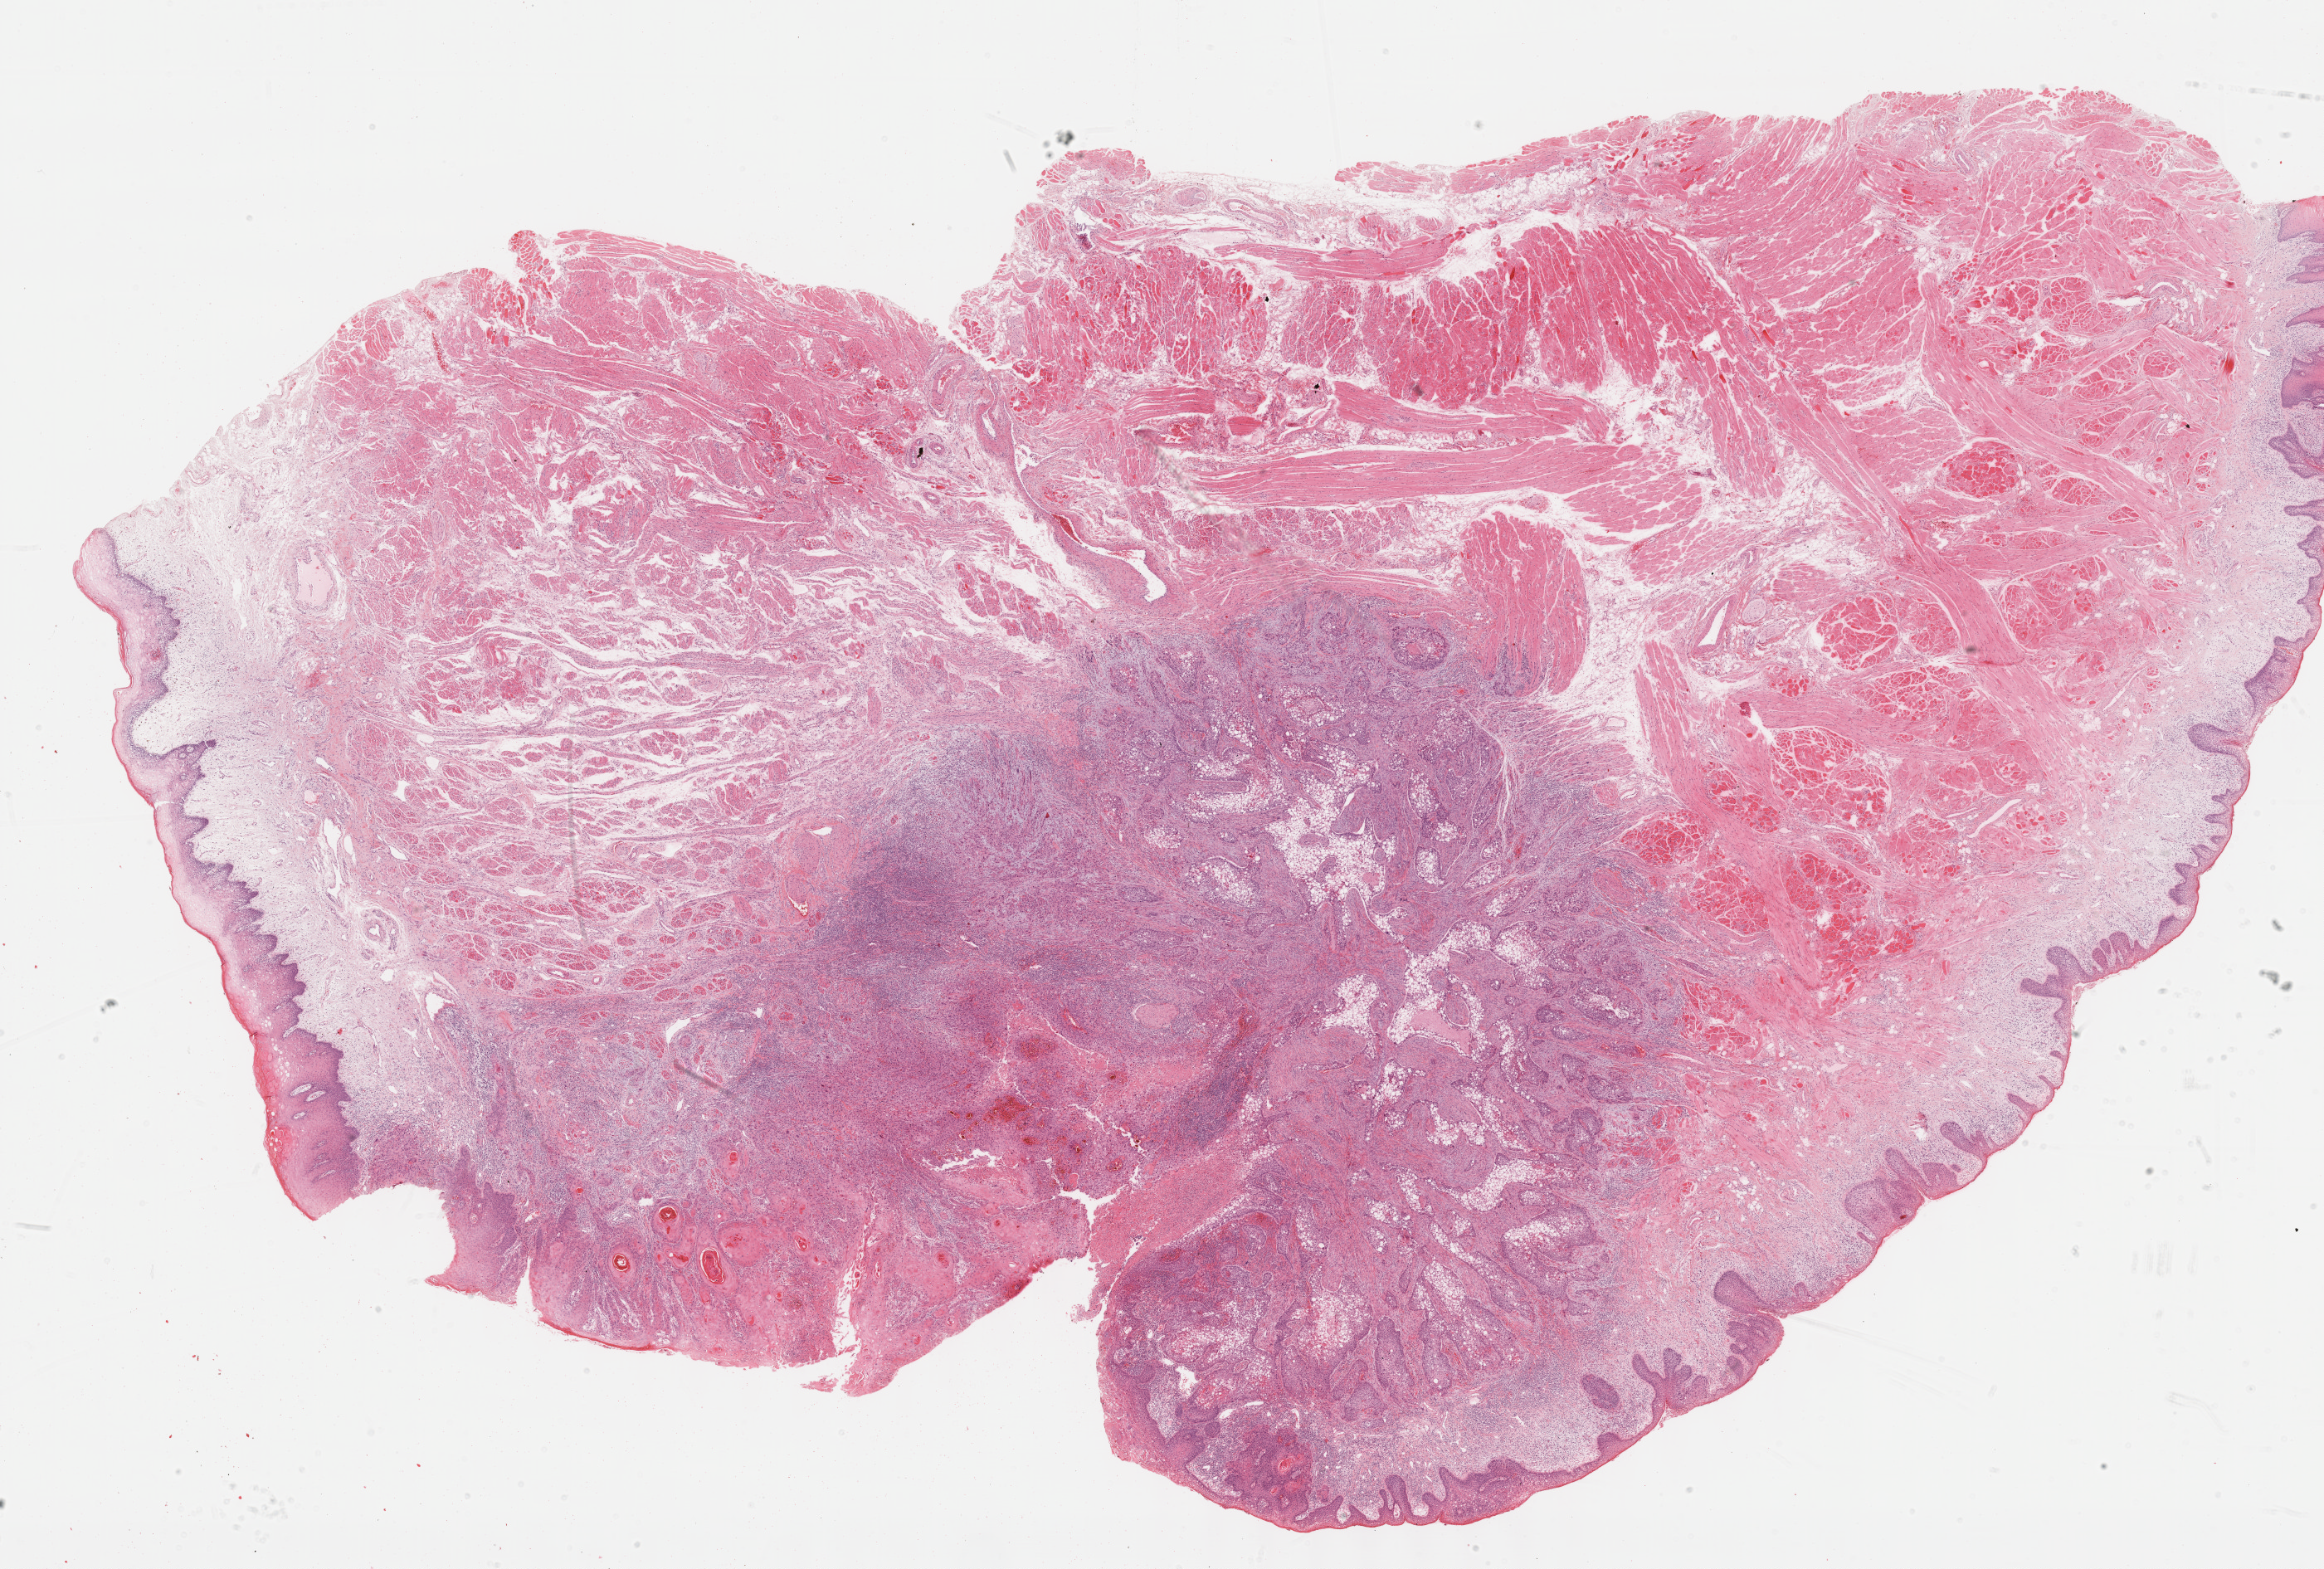
Digitized H&E tissue section (whole slide), low-resolution overview of the scanned area, about 22.6 x 15.3 mm. Formalin-fixed paraffin-embedded (FFPE) diagnostic section. Sample: primary tumour, head and neck. Male, age 49 years at initial diagnosis. Histologic grade: G2 (moderately differentiated).
* diagnosis: Squamous cell carcinoma, NOS
* AJCC pathologic stage: IVA (7th edition)